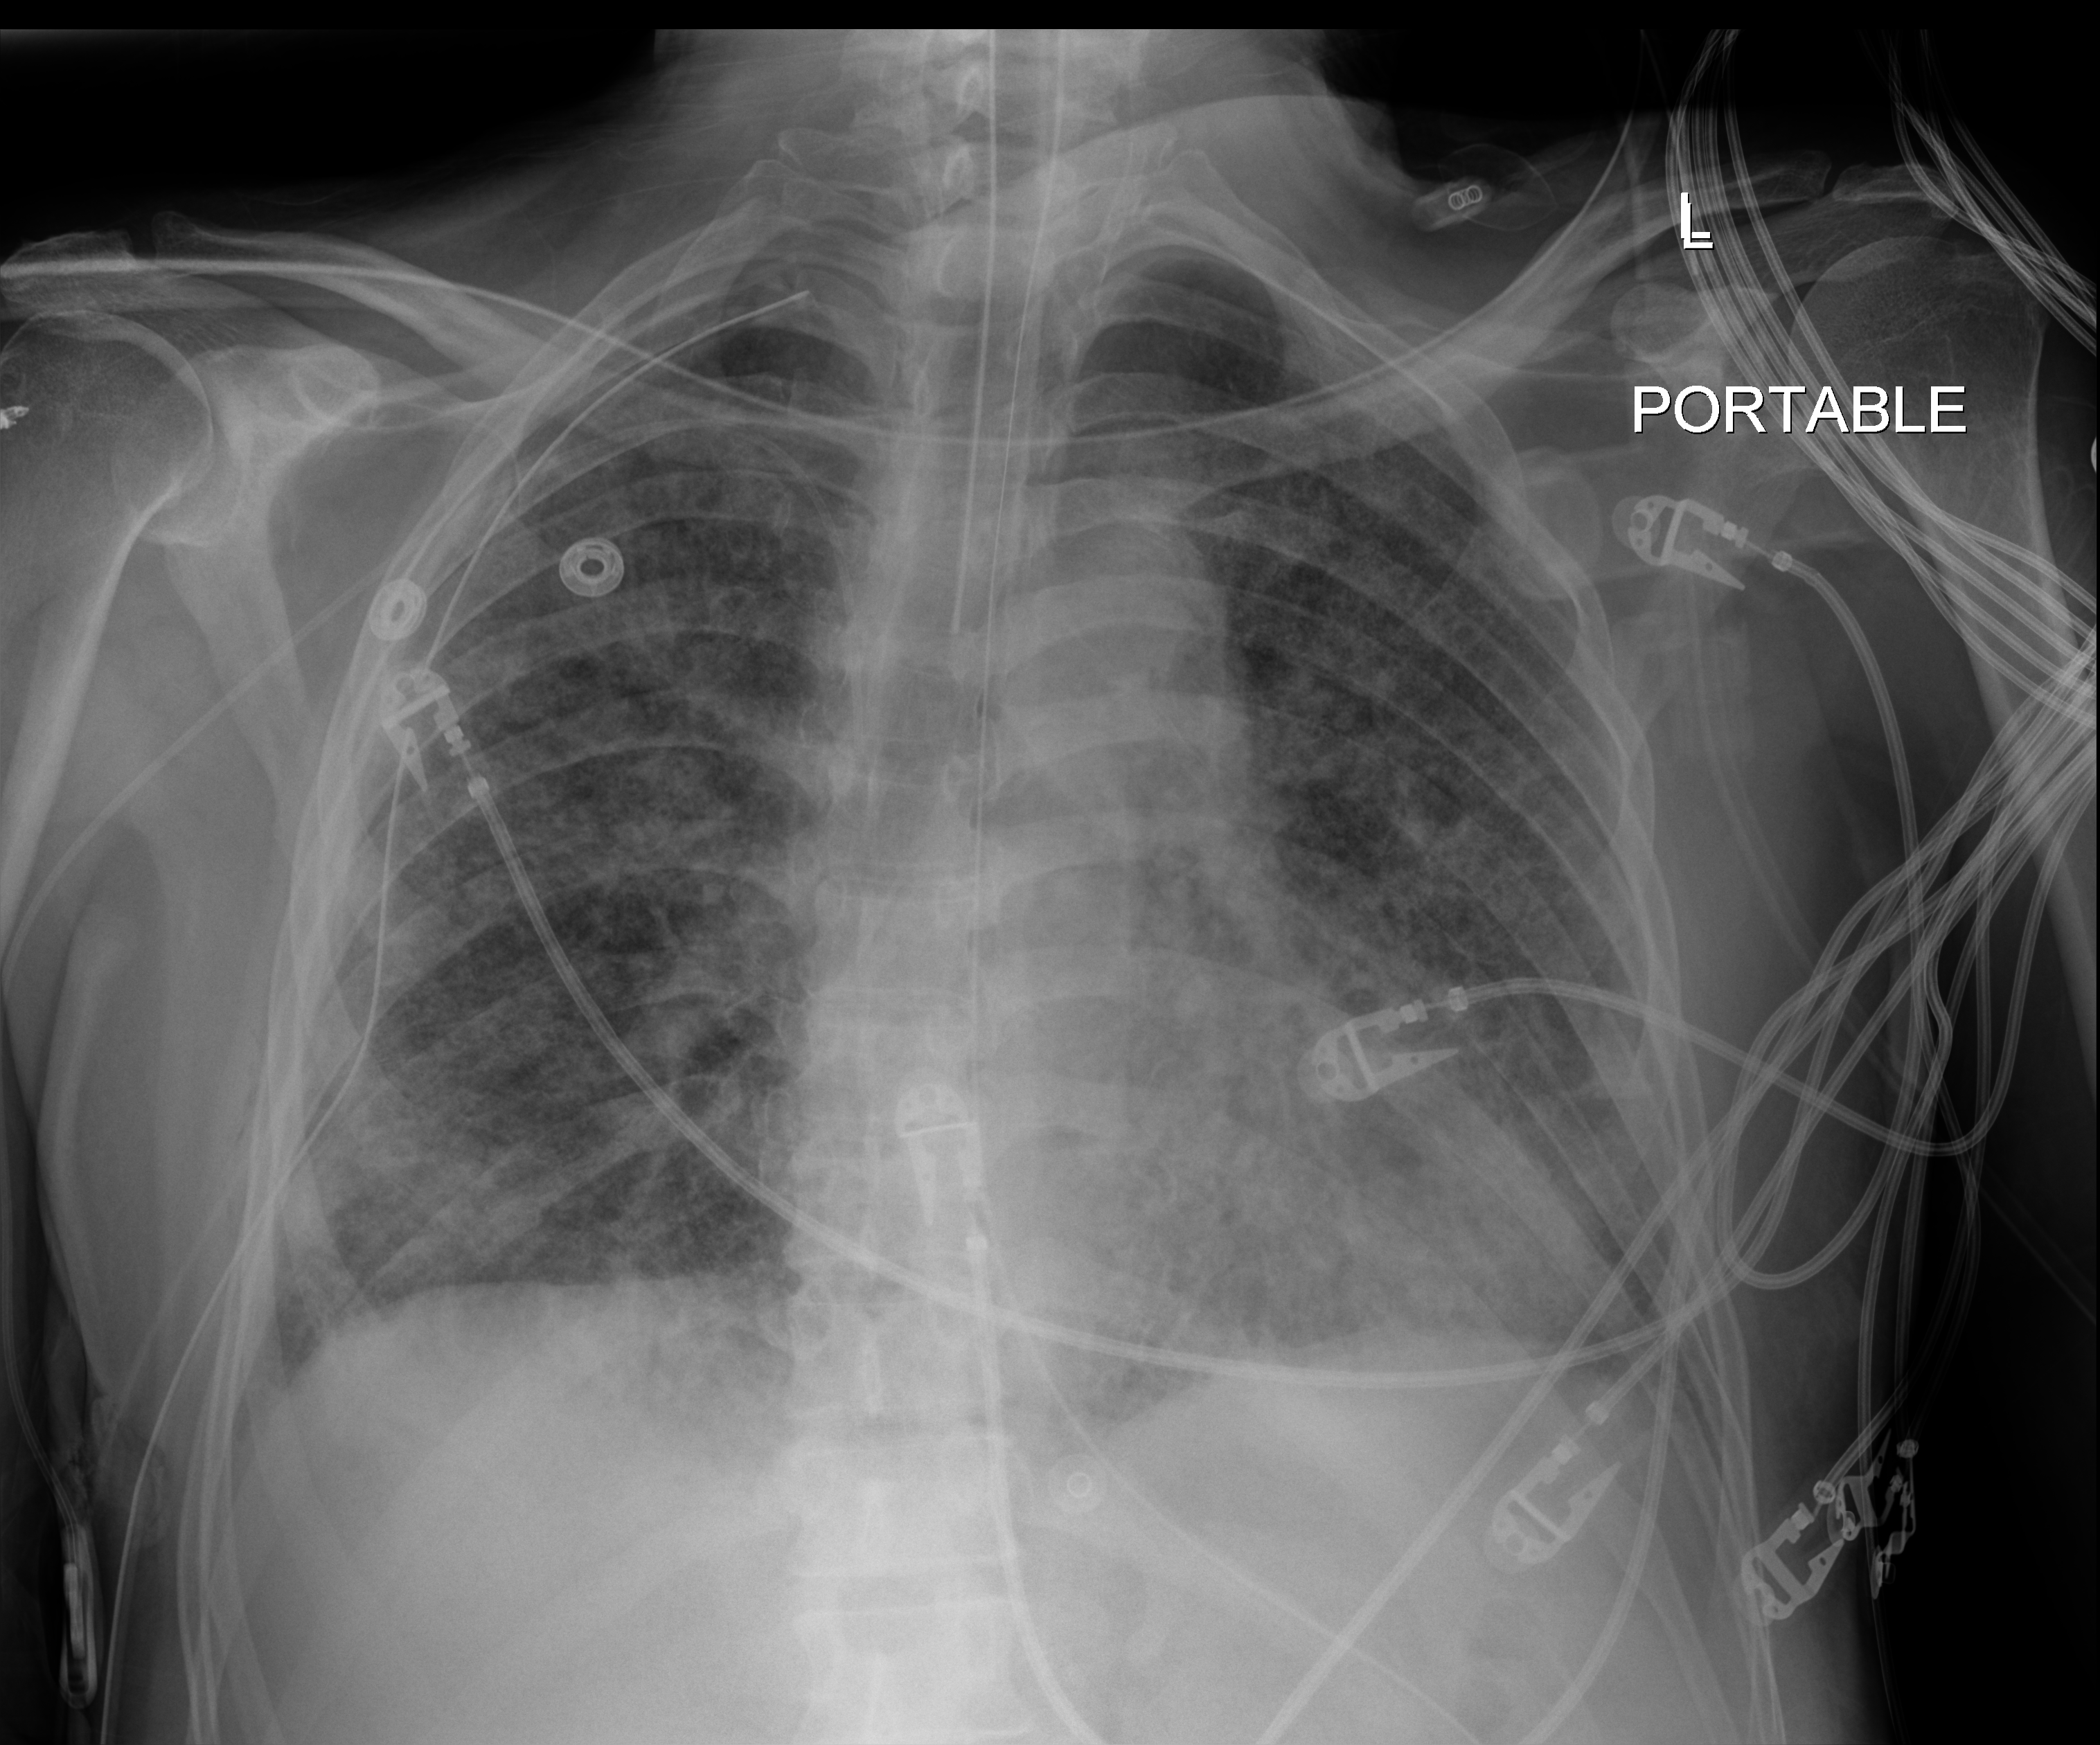
Chest radiograph. Patient hospitalised with COVID-19; male, aged 60–74 years.
Hospital-stay facts (about this admission, not read from this image; timing relative to this image not recorded):
- chronic kidney disease (admission record): no